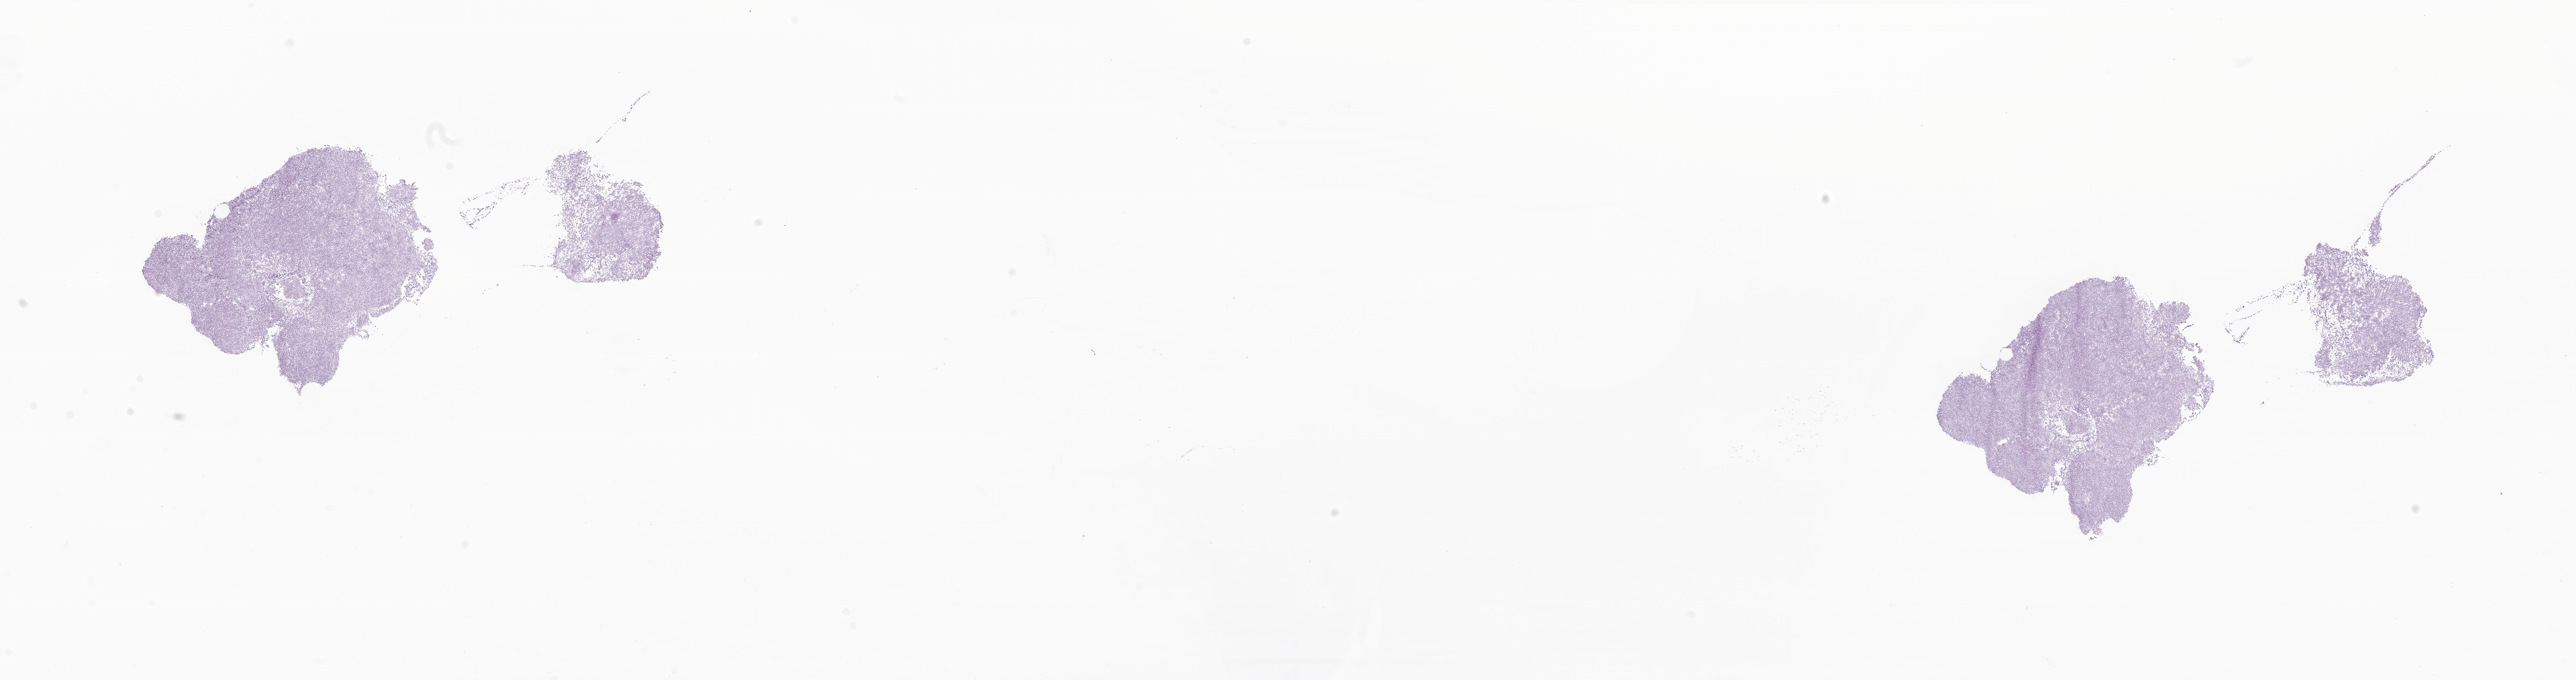
Digitized hematoxylin and eosin (H&E)-stained section of tumor tissue from the brain, a low-resolution overview of the entire scanned area, about 33.6 x 8.9 mm, cryosection (OCT / tissue freezing medium). Male patient, age 159 months.
• recorded diagnosis: Neoplasm, malignant